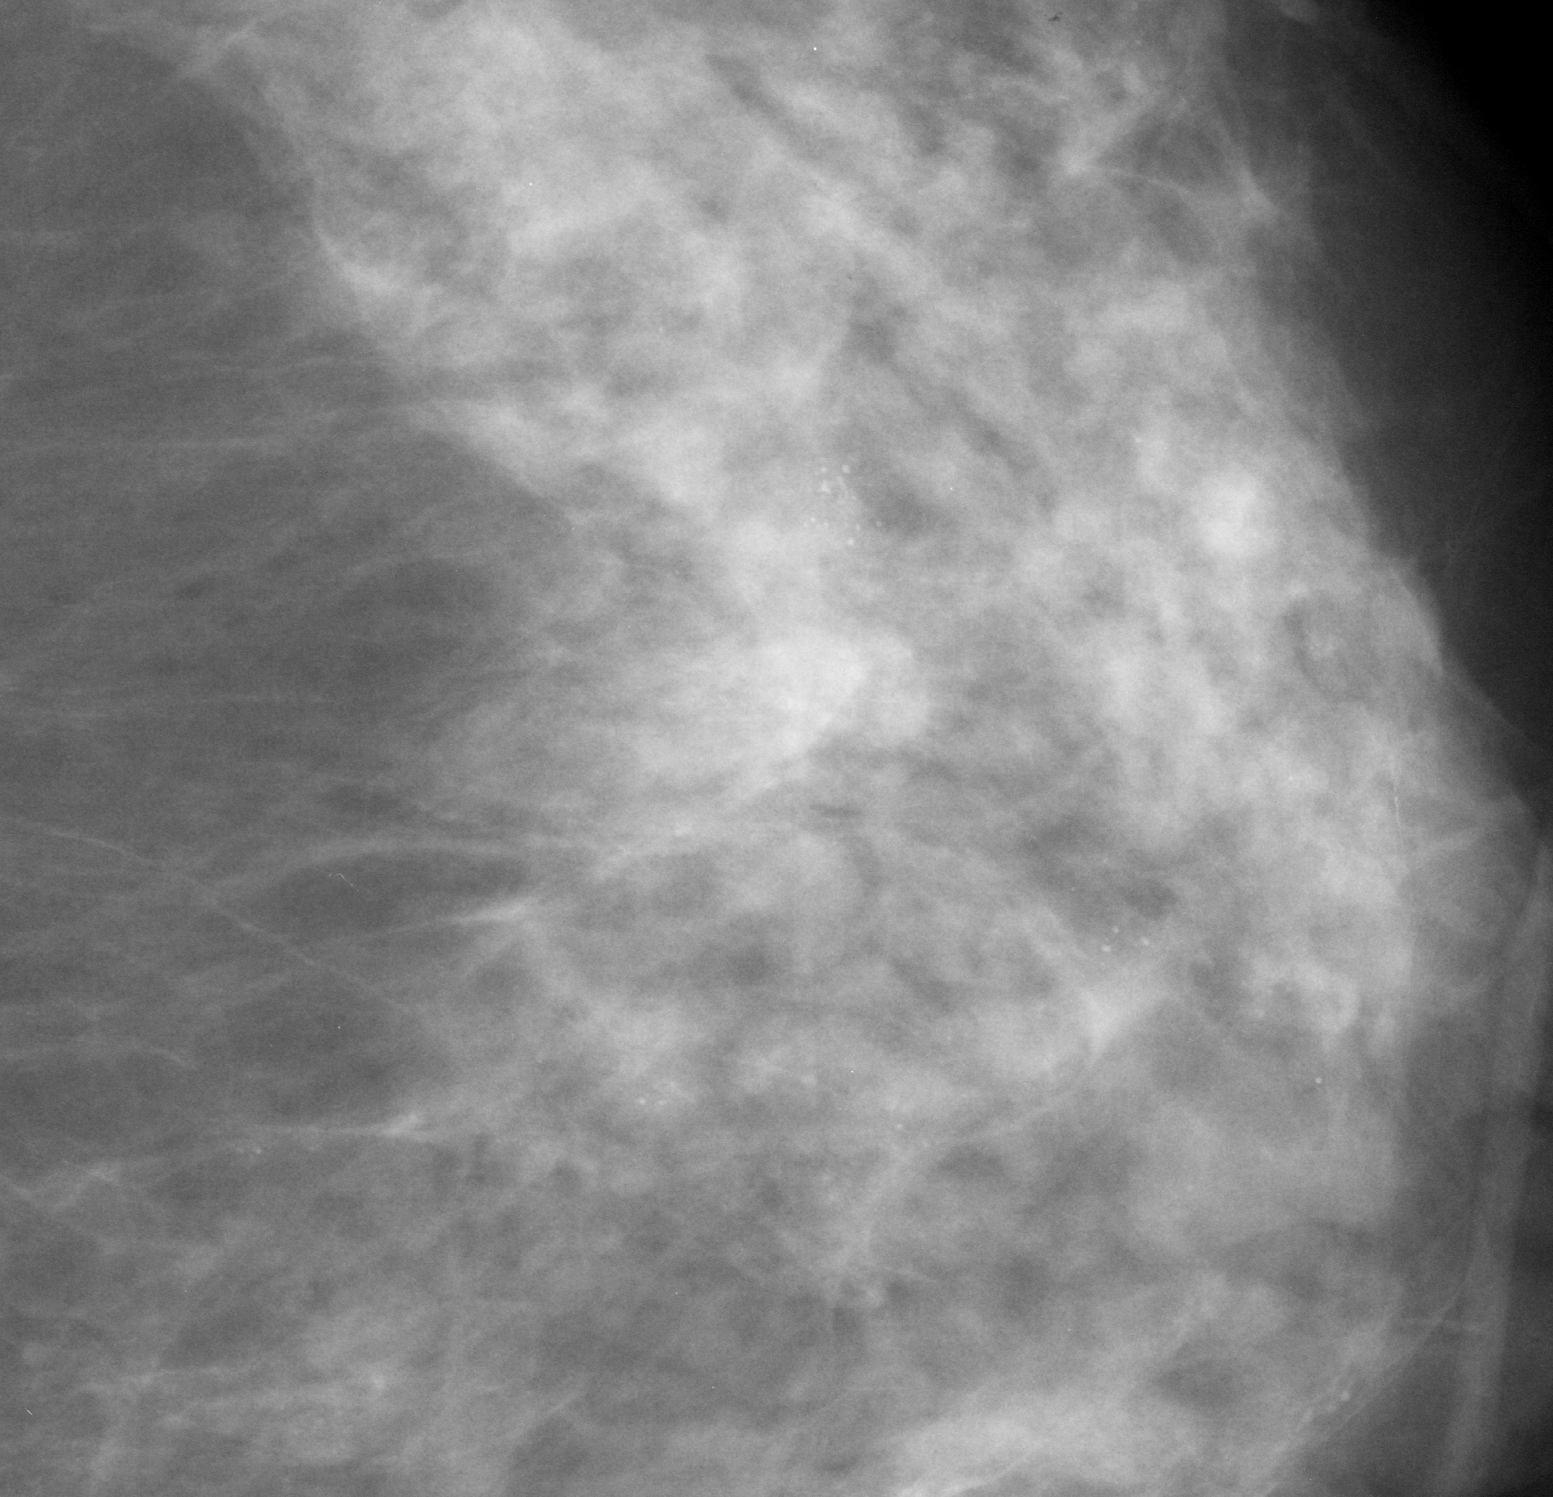
Crop from a digitized film mammogram around one marked abnormality; left breast; CC view; BI-RADS breast density category 2 (scale 1–4).
- Calcifications, morphology amorphous, distribution regional; BI-RADS assessment category 4; subtlety rating 3 on a 1 (subtle) to 5 (obvious) scale; pathology result (as recorded, not read from the image): malignant.